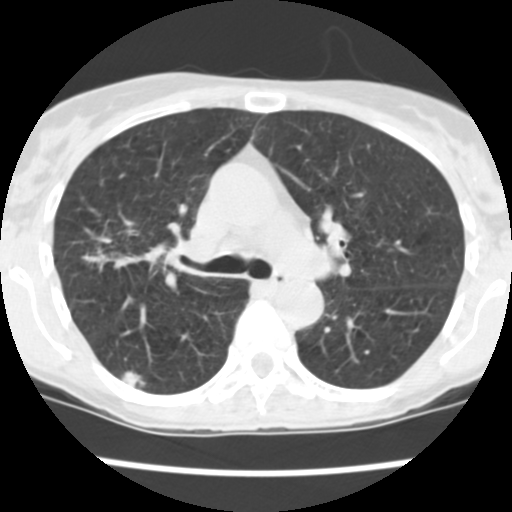
Low-dose screening chest CT, one axial slice. Slice 157 of 252 in the series (ordered by position). Lung window (W 1500 / L -600 HU). 512 × 512 image matrix, field of view 276 × 276 mm.
Annotated regions visible in this slice (expert manual segmentation):
- lesion 1 (tumor, upper lobe of right lung): box from (x=122, y=371) to (x=145, y=389) px
- lesion 2 (tumor, lower lobe of right lung): (x=85, y=250)–(x=142, y=268)